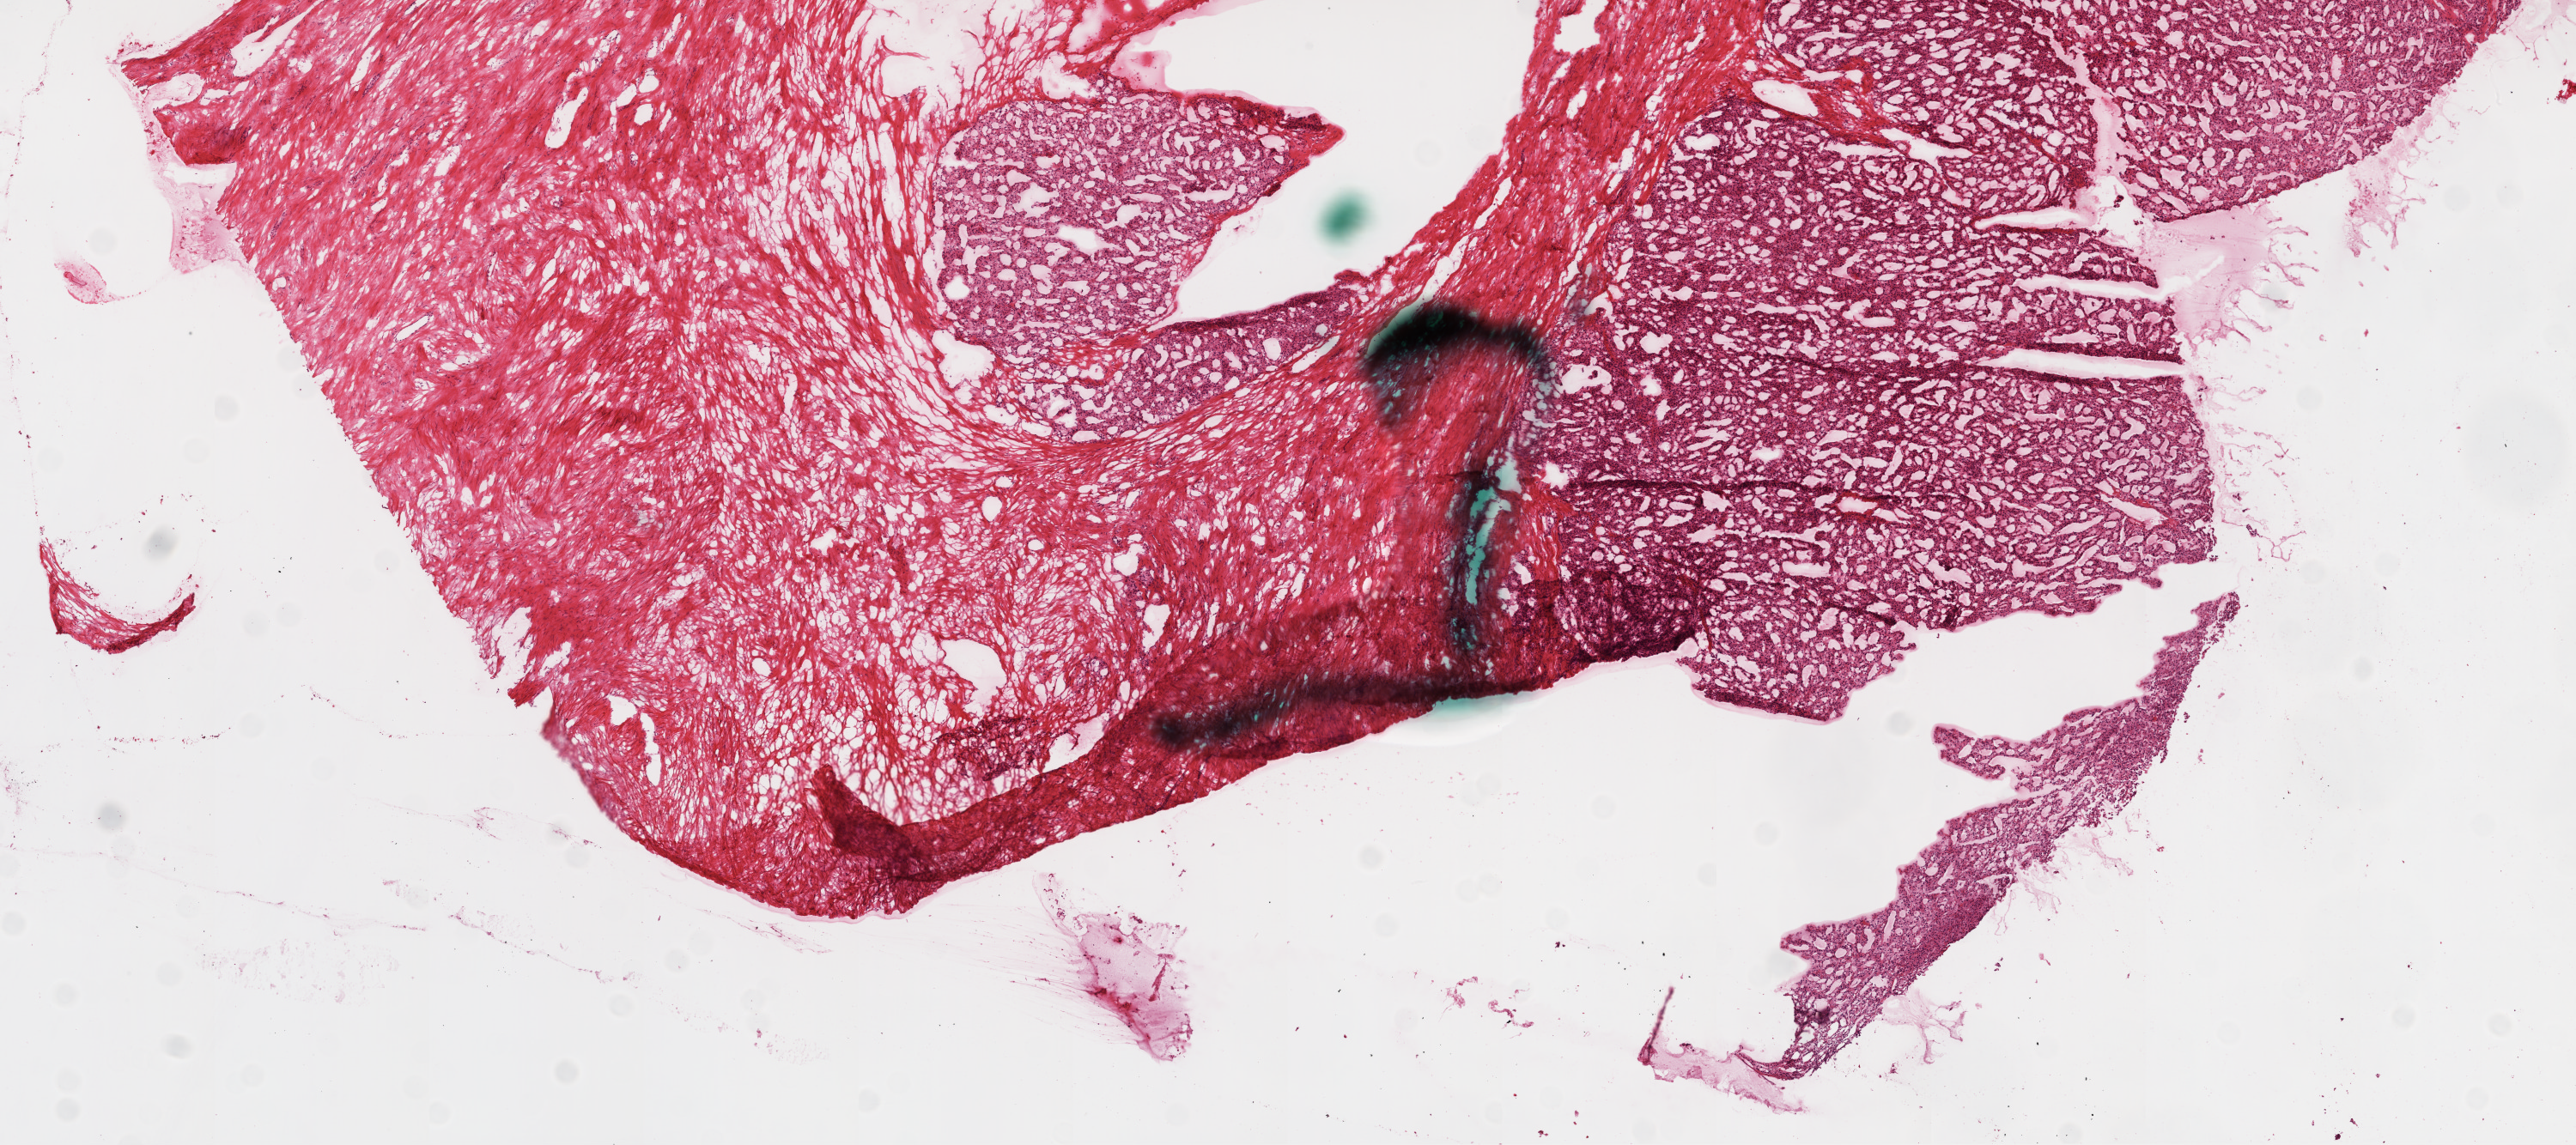
Digitized Hematoxylin and eosin (H&E) stained tissue section (whole slide) — a low-resolution overview of the entire scanned area, about 12.0 x 5.4 mm, frozen section from the top of the tissue portion, kidney, primary tumour sample. Patient: male, age at initial diagnosis 72 years. Histologic grade: G3 (poorly differentiated). Composition of this section per pathologist review: tumour cells 40%, tumour nuclei 80%, normal cells 0%, stromal cells 60%, necrosis 0%.
* laterality: right
* AJCC pathologic stage: III
* histologic diagnosis: Clear cell adenocarcinoma, NOS